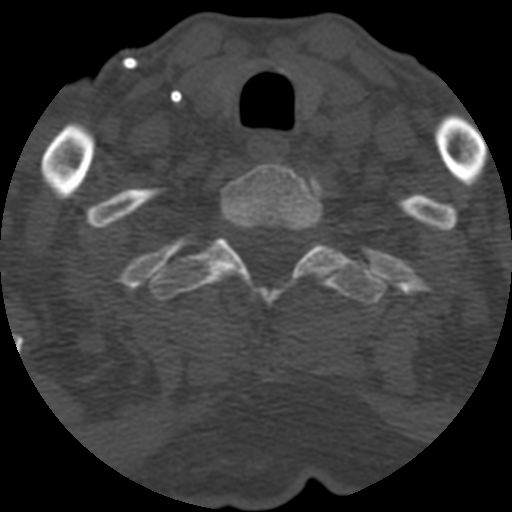
CT including the spine, one axial slice; 120 kVp; one of 3 acquisitions stored at this slice position; bone window (W 1800 / L 400 HU); 1.25 mm slice thickness; 512 × 512 image matrix, field of view 160 × 160 mm. Patient age 55 years. Case-level facts recorded for this patient, not image findings: primary cancer: colon; vertebrae with lytic lesions (as recorded): T12, L1, L5.
Structures marked on this image (semi-automatic segmentation, software-assisted and operator-edited):
- T1 vertebra: bounding box [x1, y1, x2, y2] px = [220, 164, 324, 284]
- T2 vertebra: [151, 235, 386, 307]